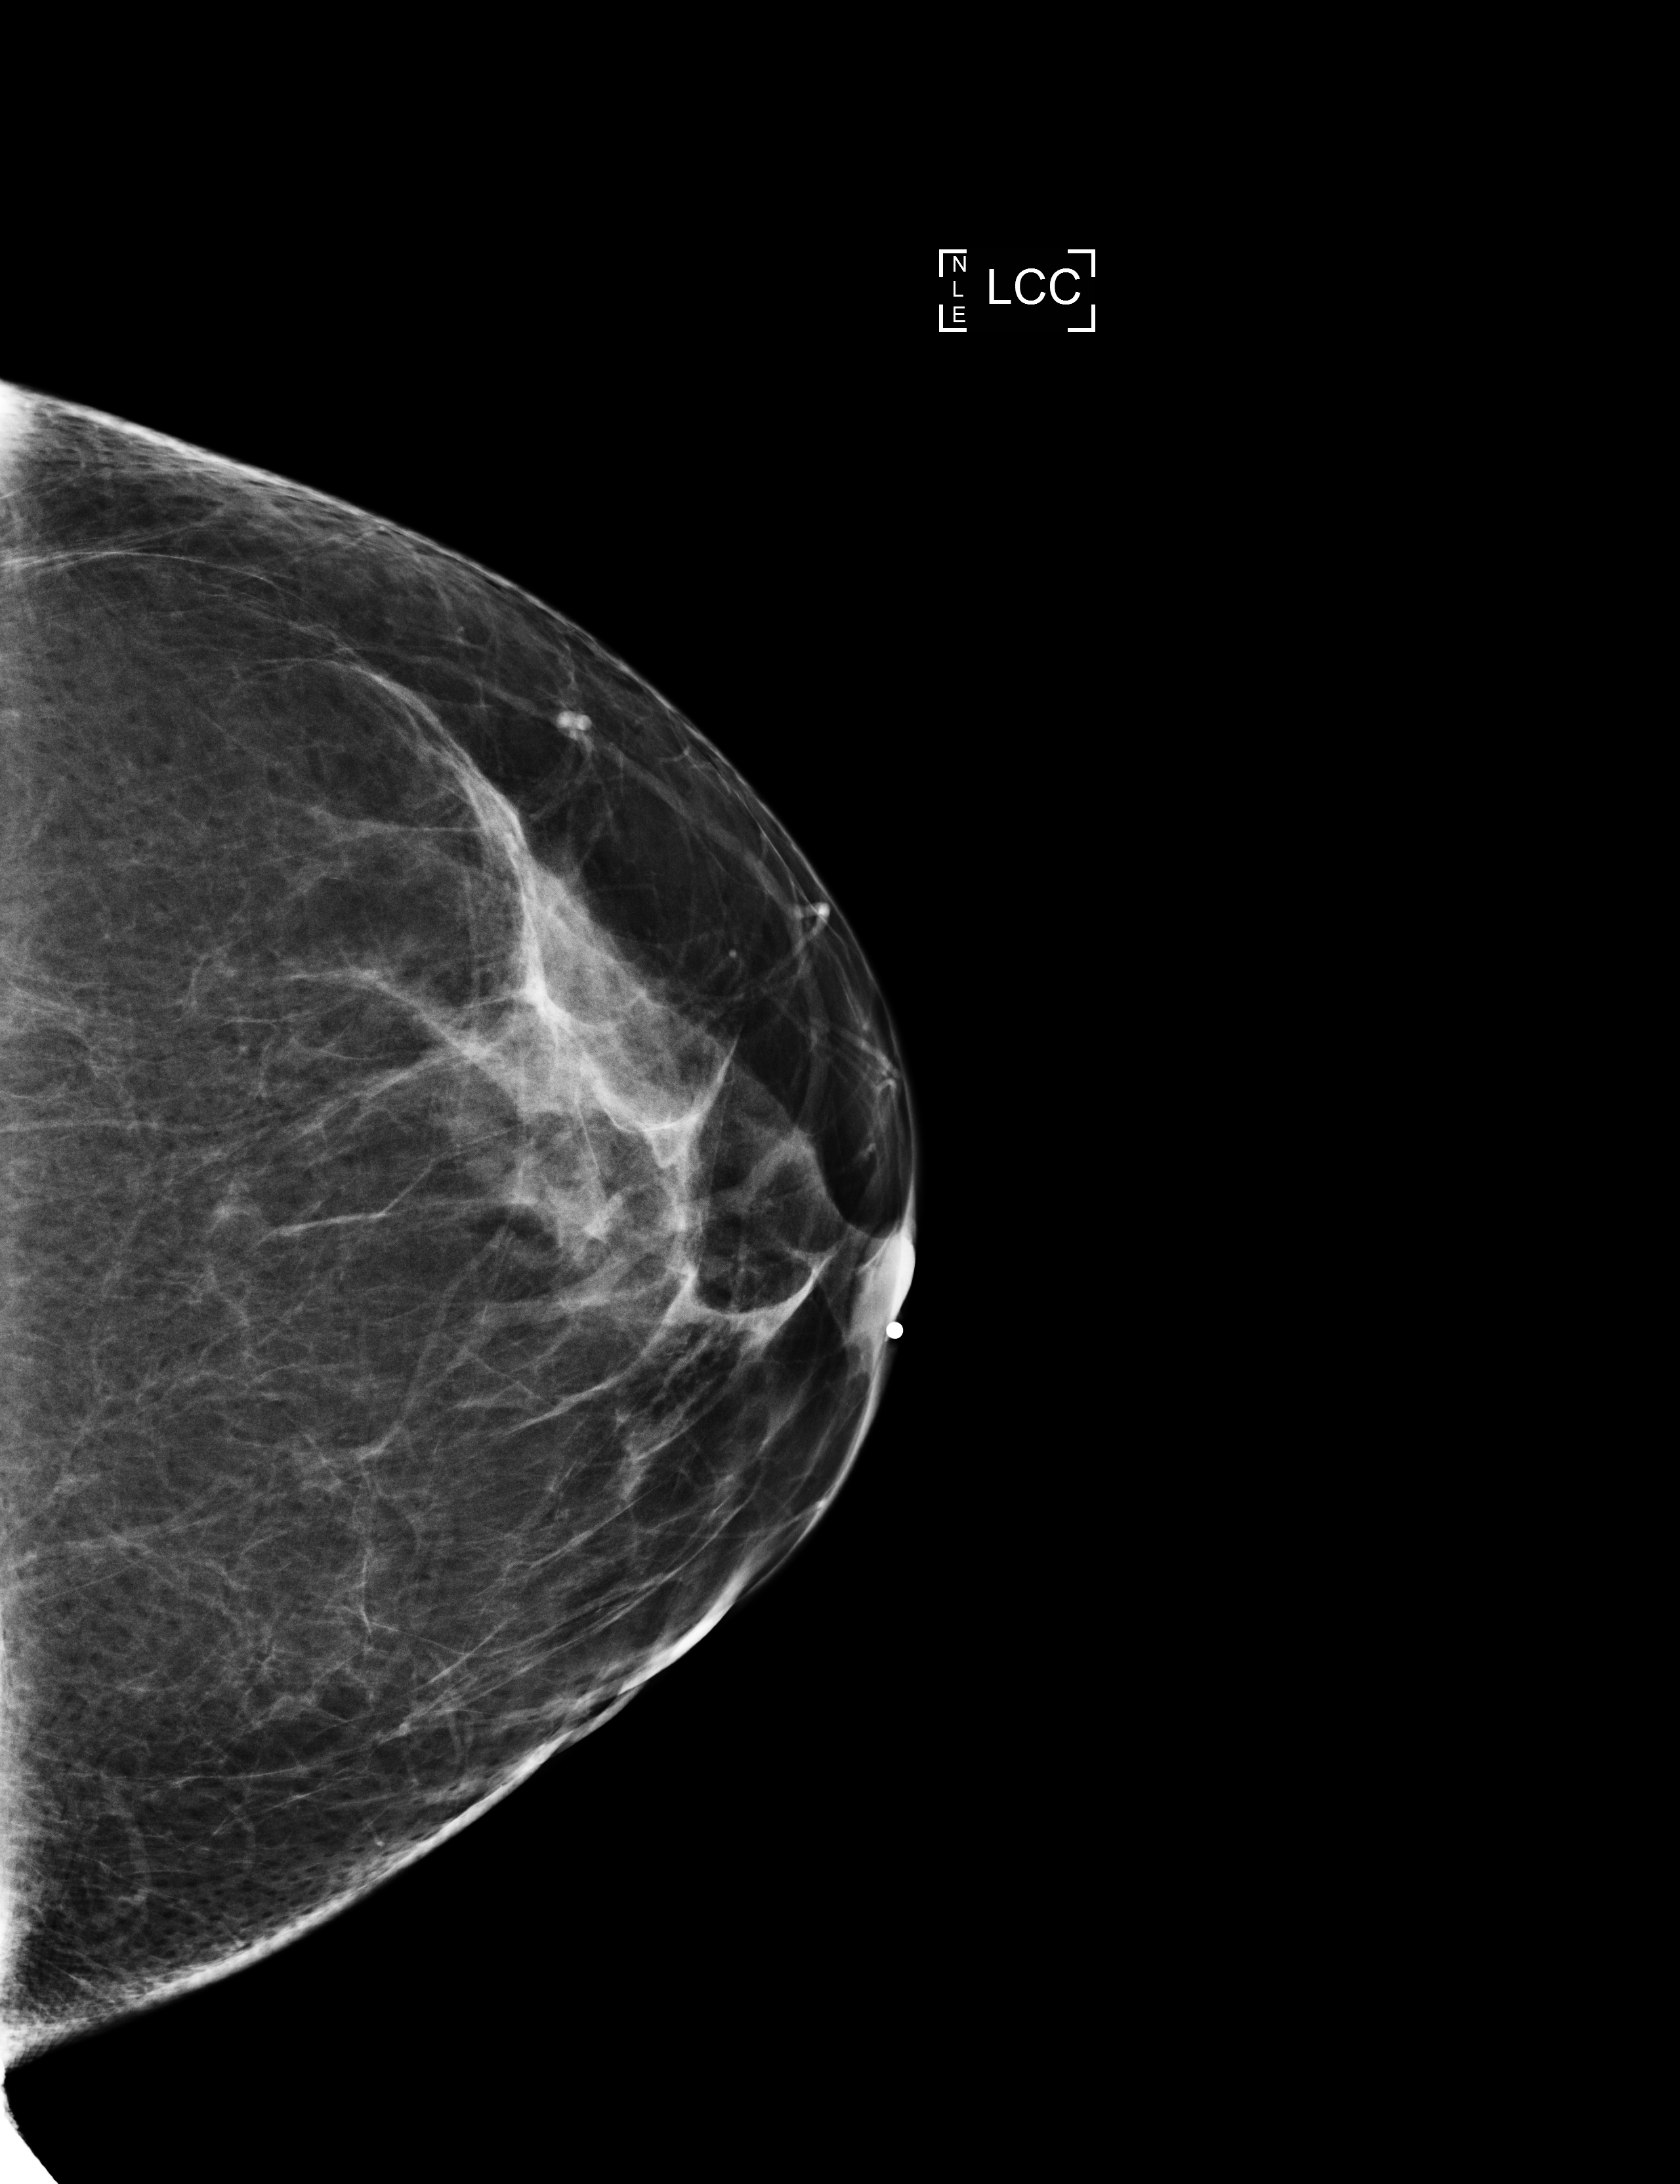
Screening examination; compressed breast thickness 71 mm; system: Selenia Dimensions.
Image type: full-field digital mammogram. Breast: left. Projection: CC view.